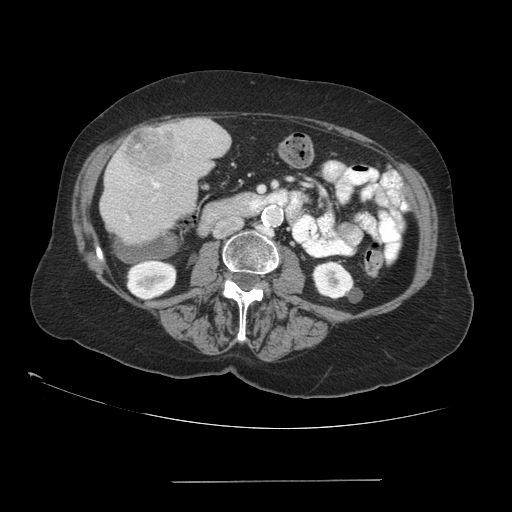
Contrast-enhanced abdominal CT (liver protocol), one axial slice; position 27 of 89 along the scan axis; reconstruction kernel STANDARD; 140 kVp; soft-tissue window (W 400 / L 40 HU); 512 × 512 image matrix, field of view 400 × 400 mm. Case-level facts recorded for this patient, not image findings: diagnosis: hepatocellular carcinoma (patient treated with transarterial chemoembolisation; whether this scan precedes or follows treatment is not stated here); TNM stage (as recorded): Stage-IVA; Child-Pugh class: A; tumour differentiation: poorly differentiated; tumour nodularity: uninodular.
Outlined on this slice (semi-automatically segmented with operator editing):
- liver parenchyma outside the tumour (the mass and vessels are separate outlines, so this box may not span the whole liver): bounding box (x1, y1, x2, y2) in pixels: (100, 118, 230, 244)
- mass: (123, 125, 175, 171)
- liver vessels: (127, 182, 159, 219)